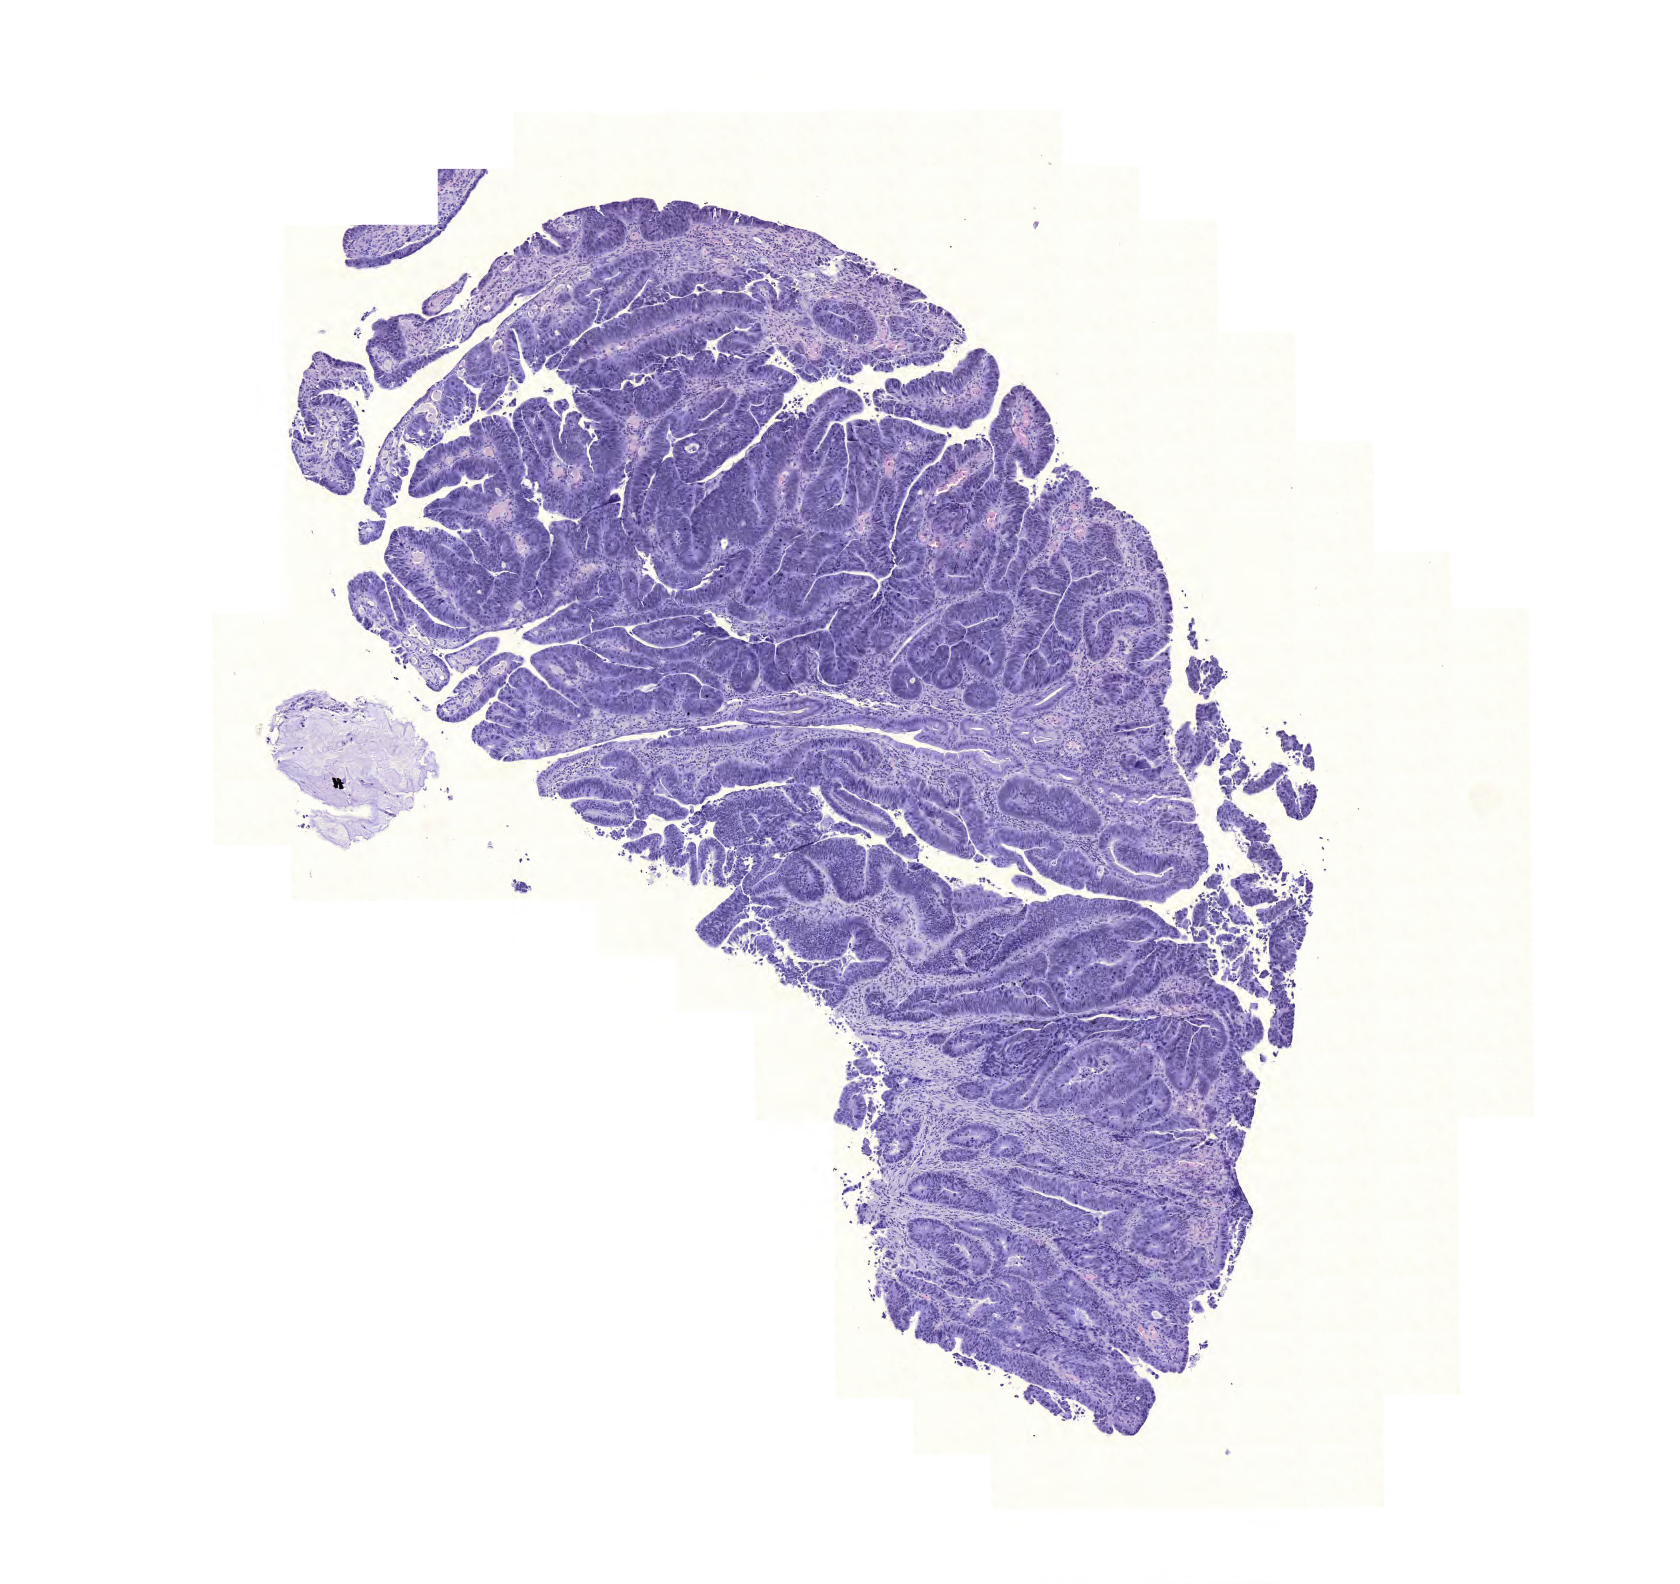
Whole-slide histology image, Hematoxylin and eosin (H&E) stained — shown as a low-resolution overview of the whole scanned area (about 6.2 x 5.9 mm). Formalin-fixed paraffin-embedded (FFPE) diagnostic section. Sample: primary tumour, colon. Male, age 67 years at initial diagnosis.
Diagnosis: Adenocarcinoma, NOS.